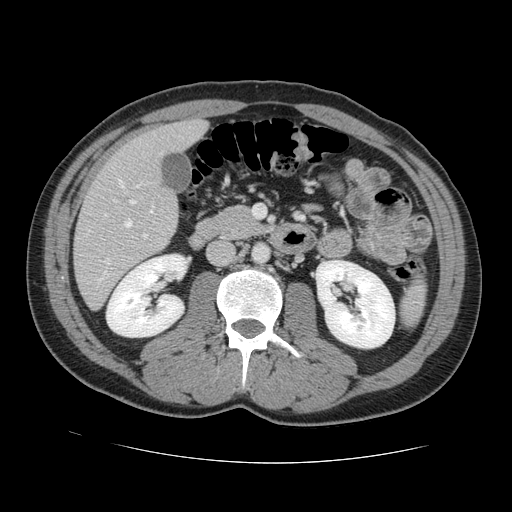
Contrast-enhanced abdominal CT, one axial slice; slice 52 of 131 in the series (ordered by position); 120 kVp; intravenous contrast given; soft-tissue window (W 400 / L 40 HU); 2.5 mm slice thickness; 512 × 512 image matrix, field of view 380 × 380 mm. Male patient, age 40 years. Case-level facts recorded for this patient, not image findings: diagnosis: colorectal cancer liver metastases, imaged before liver resection; multiple liver metastases: yes; largest metastasis: 2.9 cm; chemotherapy before resection: yes.
Annotated regions visible in this slice (manually delineated by an expert):
- hepatic veins: bounding box <104,180,153,264> (left, top, right, bottom; pixels)
- liver: <75,121,206,308>
- planned liver remnant (the part of the liver to remain after resection): <118,121,206,171>
- portal vein (with intrahepatic branches): <130,200,148,238>